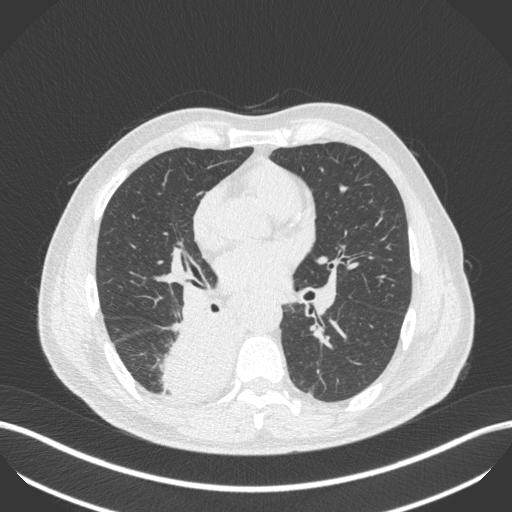
Chest CT, one axial slice. Position 242 of 451 along the scan axis. 100 kVp. Lung window (W 1500 / L -600 HU). 512 × 512 image matrix. Male patient, age 61 years. From the clinical record (not read from this slice): clinical TNM (as recorded): T1 N0 M0; histopathological grade: G3.
Annotated regions visible in this slice (bounding box drawn by a radiologist):
- lung tumour (recorded histology: small cell carcinoma): bounding box [x1, y1, x2, y2] px = [155, 308, 235, 400]